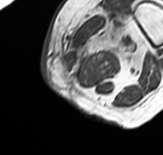
MRI of an extremity soft-tissue mass, one axial slice; position 10 of 65 along the scan axis; MR volume resampled by the dataset authors to the PET/CT grid (not the native acquisition matrix); 163 × 155 image matrix, field of view 159 × 151 mm. Female patient. Case-level facts recorded for this patient, not image findings: histological type: pleomorphic leiomyosarcoma; grade: high; site of the primary tumour: left thigh.
Annotated regions visible in this slice (expert contour drawn on MRI and transferred to this co-registered scan by the dataset authors):
- gross tumour volume including surrounding oedema: bounding box [x1, y1, x2, y2] px = [62, 8, 145, 80]